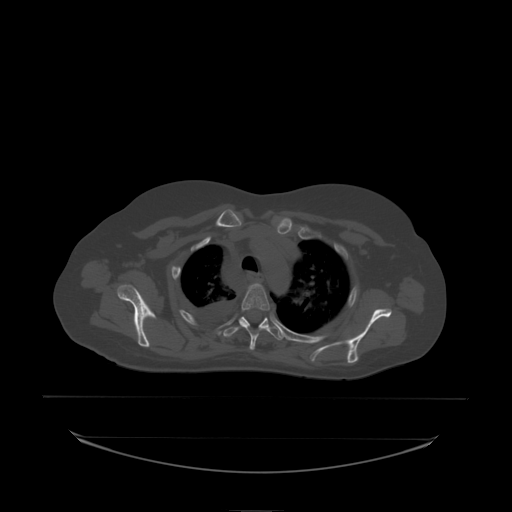
CT including the spine, one axial slice. Slice 171 of 242 in the series (ordered by position). Bone window (W 1800 / L 400 HU). 2.5 mm slice thickness. 512 × 512 image matrix. Female patient, age 53 years. Case-level facts recorded for this patient, not image findings: primary cancer: lung; vertebrae with lytic lesions (as recorded): T7, L1.
Outlined on this slice (semi-automatically segmented with operator editing):
- T3 vertebra: bounding box (x1, y1, x2, y2) in pixels: (242, 284, 270, 338)
- T4 vertebra: (225, 317, 280, 338)